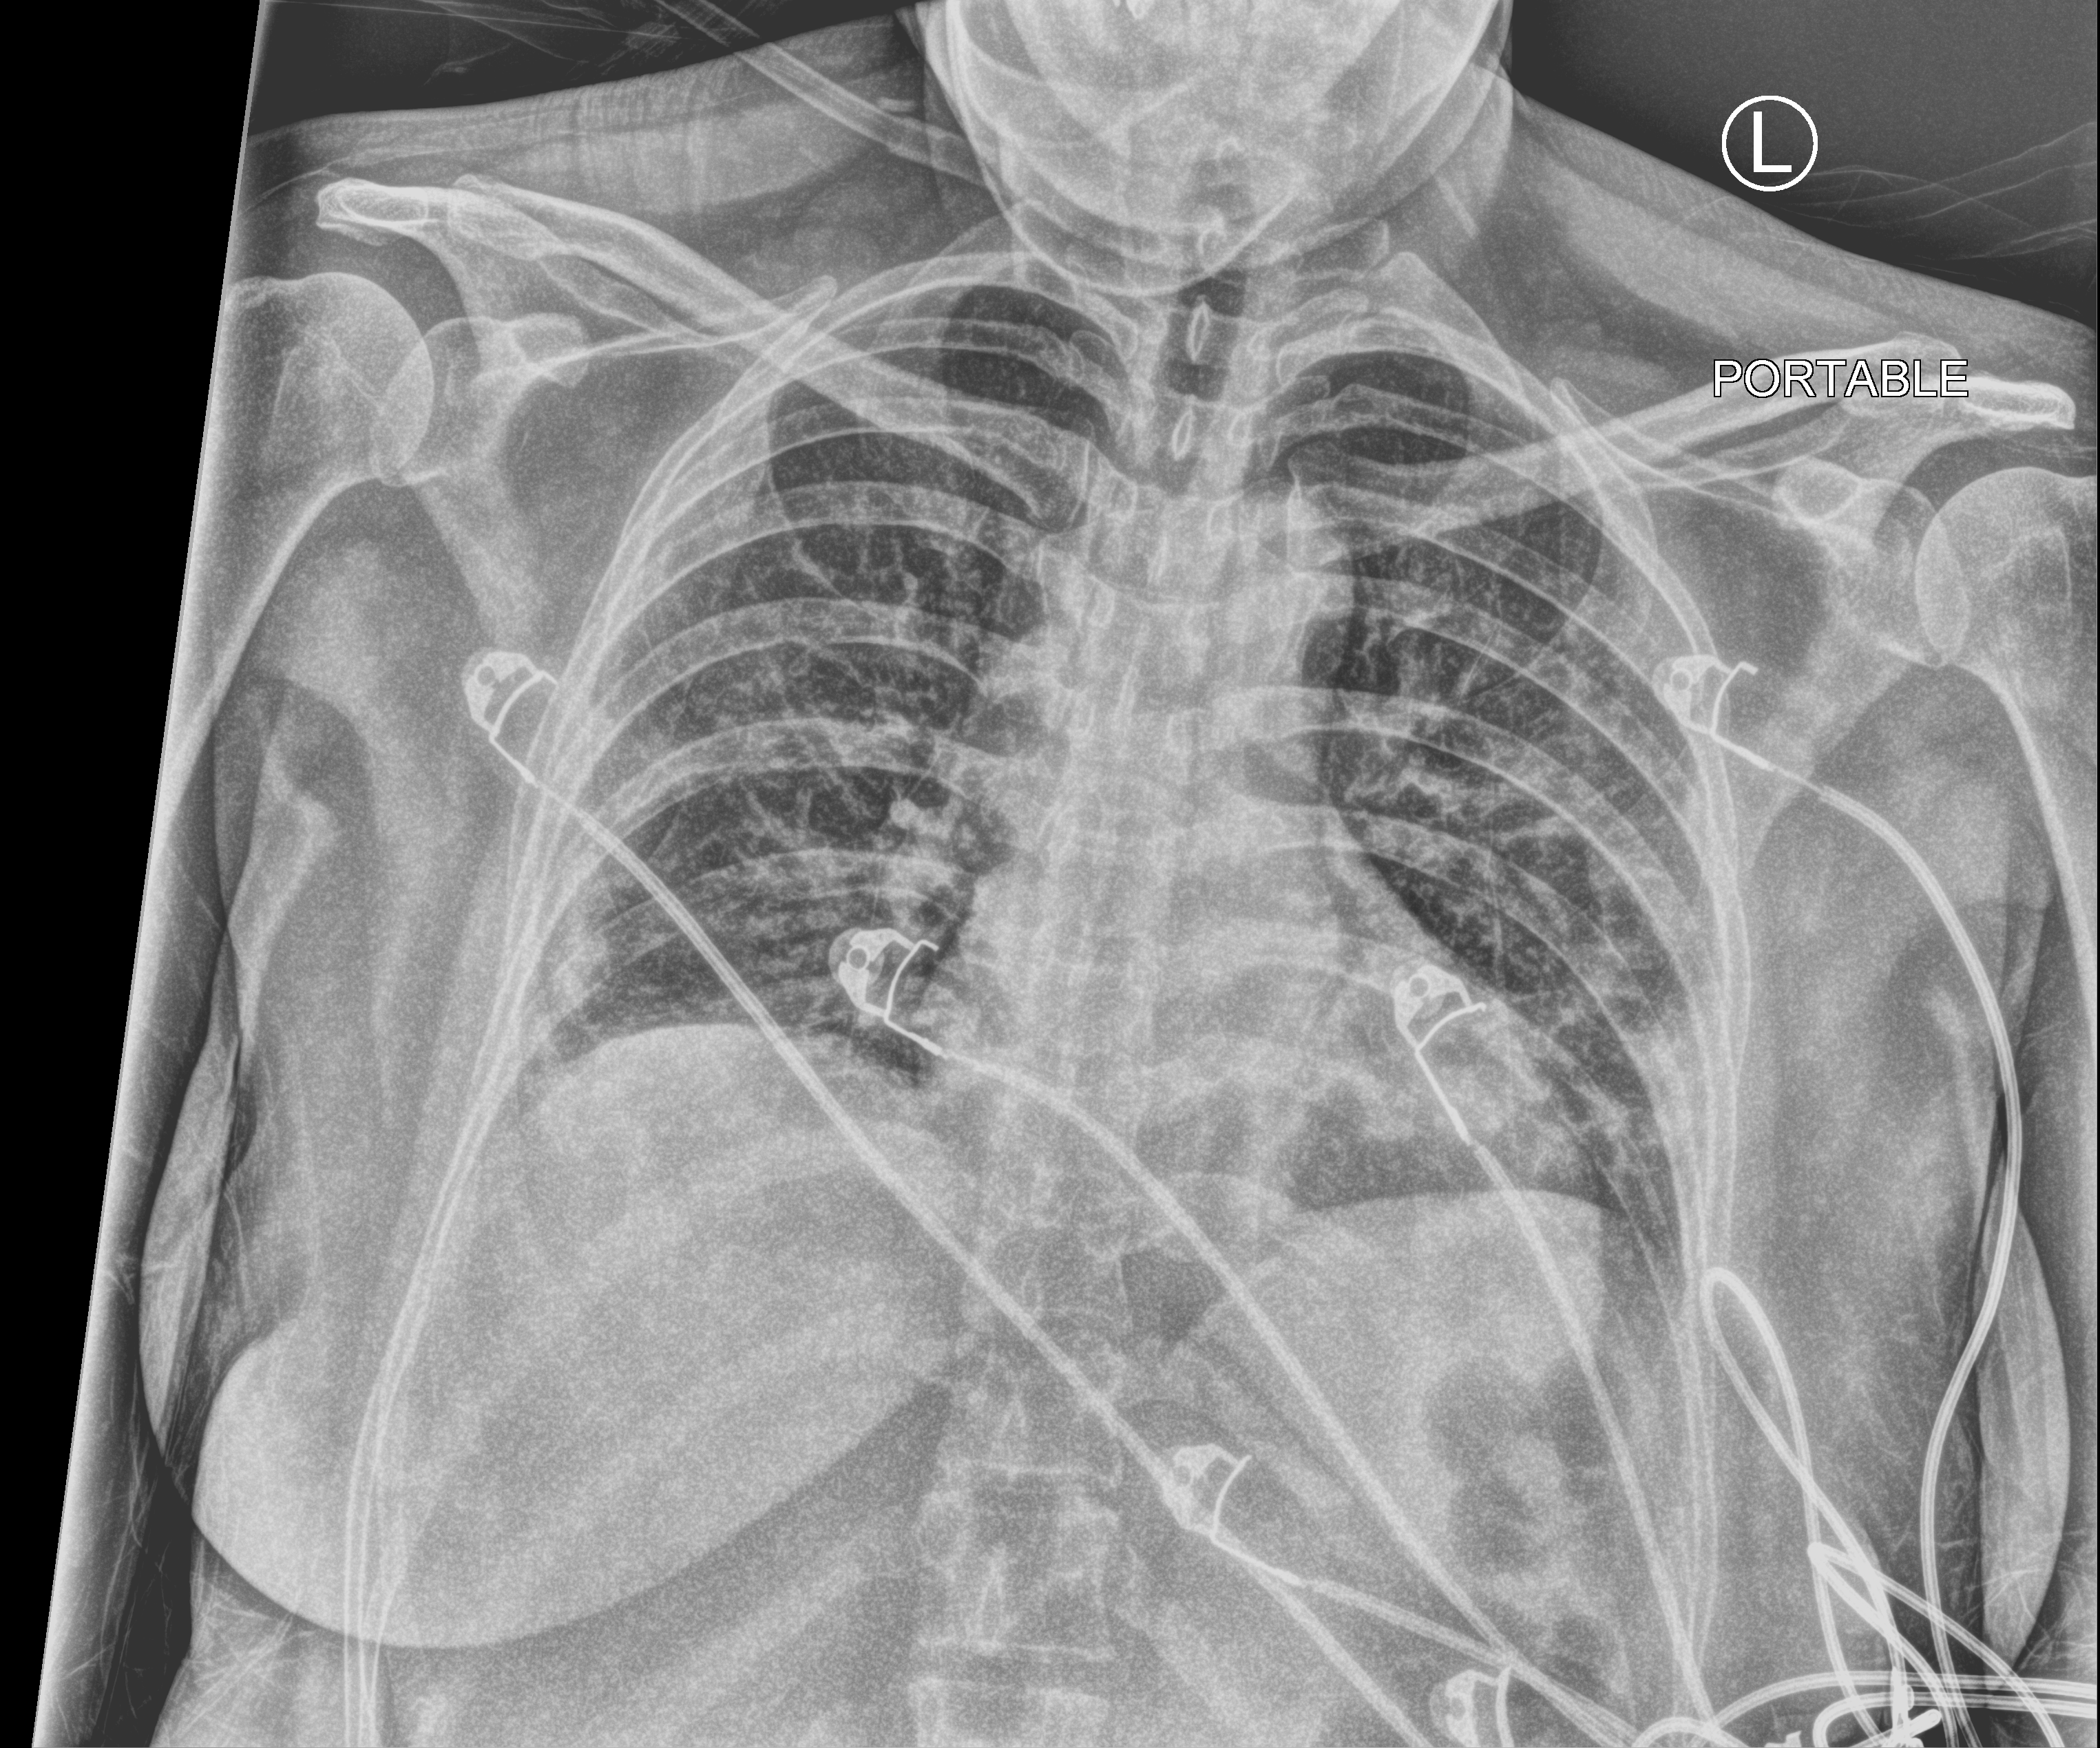
Bedside chest radiograph (computed radiography). Patient hospitalised with COVID-19; female, aged 18–59 years.
From the hospital-stay record, not from the radiograph (when in the stay this image was taken is not recorded):
- smoking status (admission record): never
- mechanically ventilated during this hospital stay: no
- admitted to intensive care during this hospital stay: no